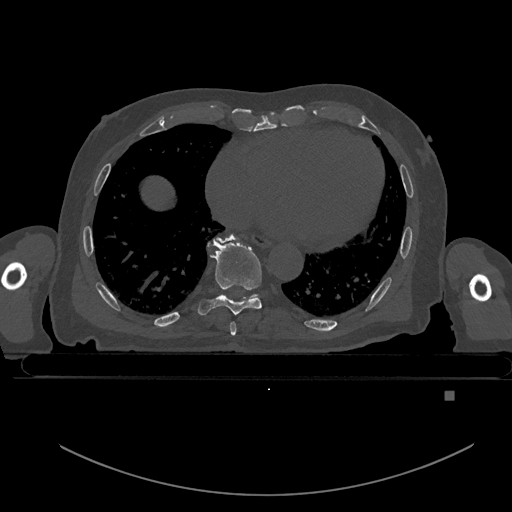
CT including the spine, one axial slice; position 198 of 969 along the scan axis; bone window (W 1800 / L 400 HU); 0.5 mm slice thickness; 512 × 512 image matrix, field of view 456 × 456 mm. Patient: male, 82 years. Case-level facts recorded for this patient, not image findings: primary cancer: prostate.
Annotated regions visible in this slice (semi-automatically segmented with operator editing):
- T7 vertebra: bounding box <230,321,236,336> (left, top, right, bottom; pixels)
- T8 vertebra: <198,236,270,317>
- T9 vertebra: <216,235,256,297>